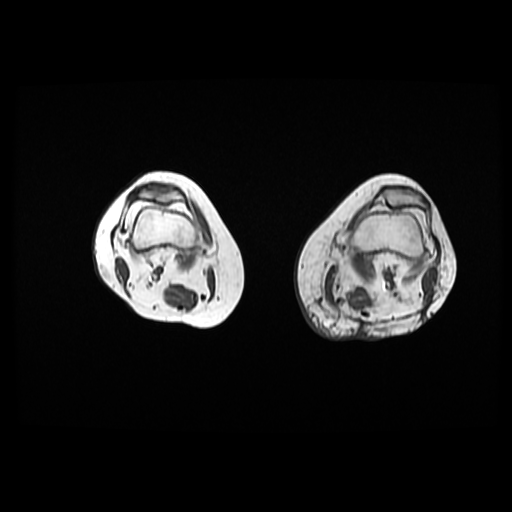
MRI of an extremity soft-tissue mass, one axial slice. Position 12 of 42 along the scan axis. 6 mm slice thickness. 512 × 512 image matrix, field of view 420 × 420 mm. Female patient. Case-level facts recorded for this patient, not image findings: histological type: pleomorphic leiomyosarcoma; grade: high; site of the primary tumour: left thigh.
Outlined on this slice (manually delineated by an expert):
- gross tumour volume including surrounding oedema: bounding box (x1, y1, x2, y2) in pixels: (323, 260, 342, 302)